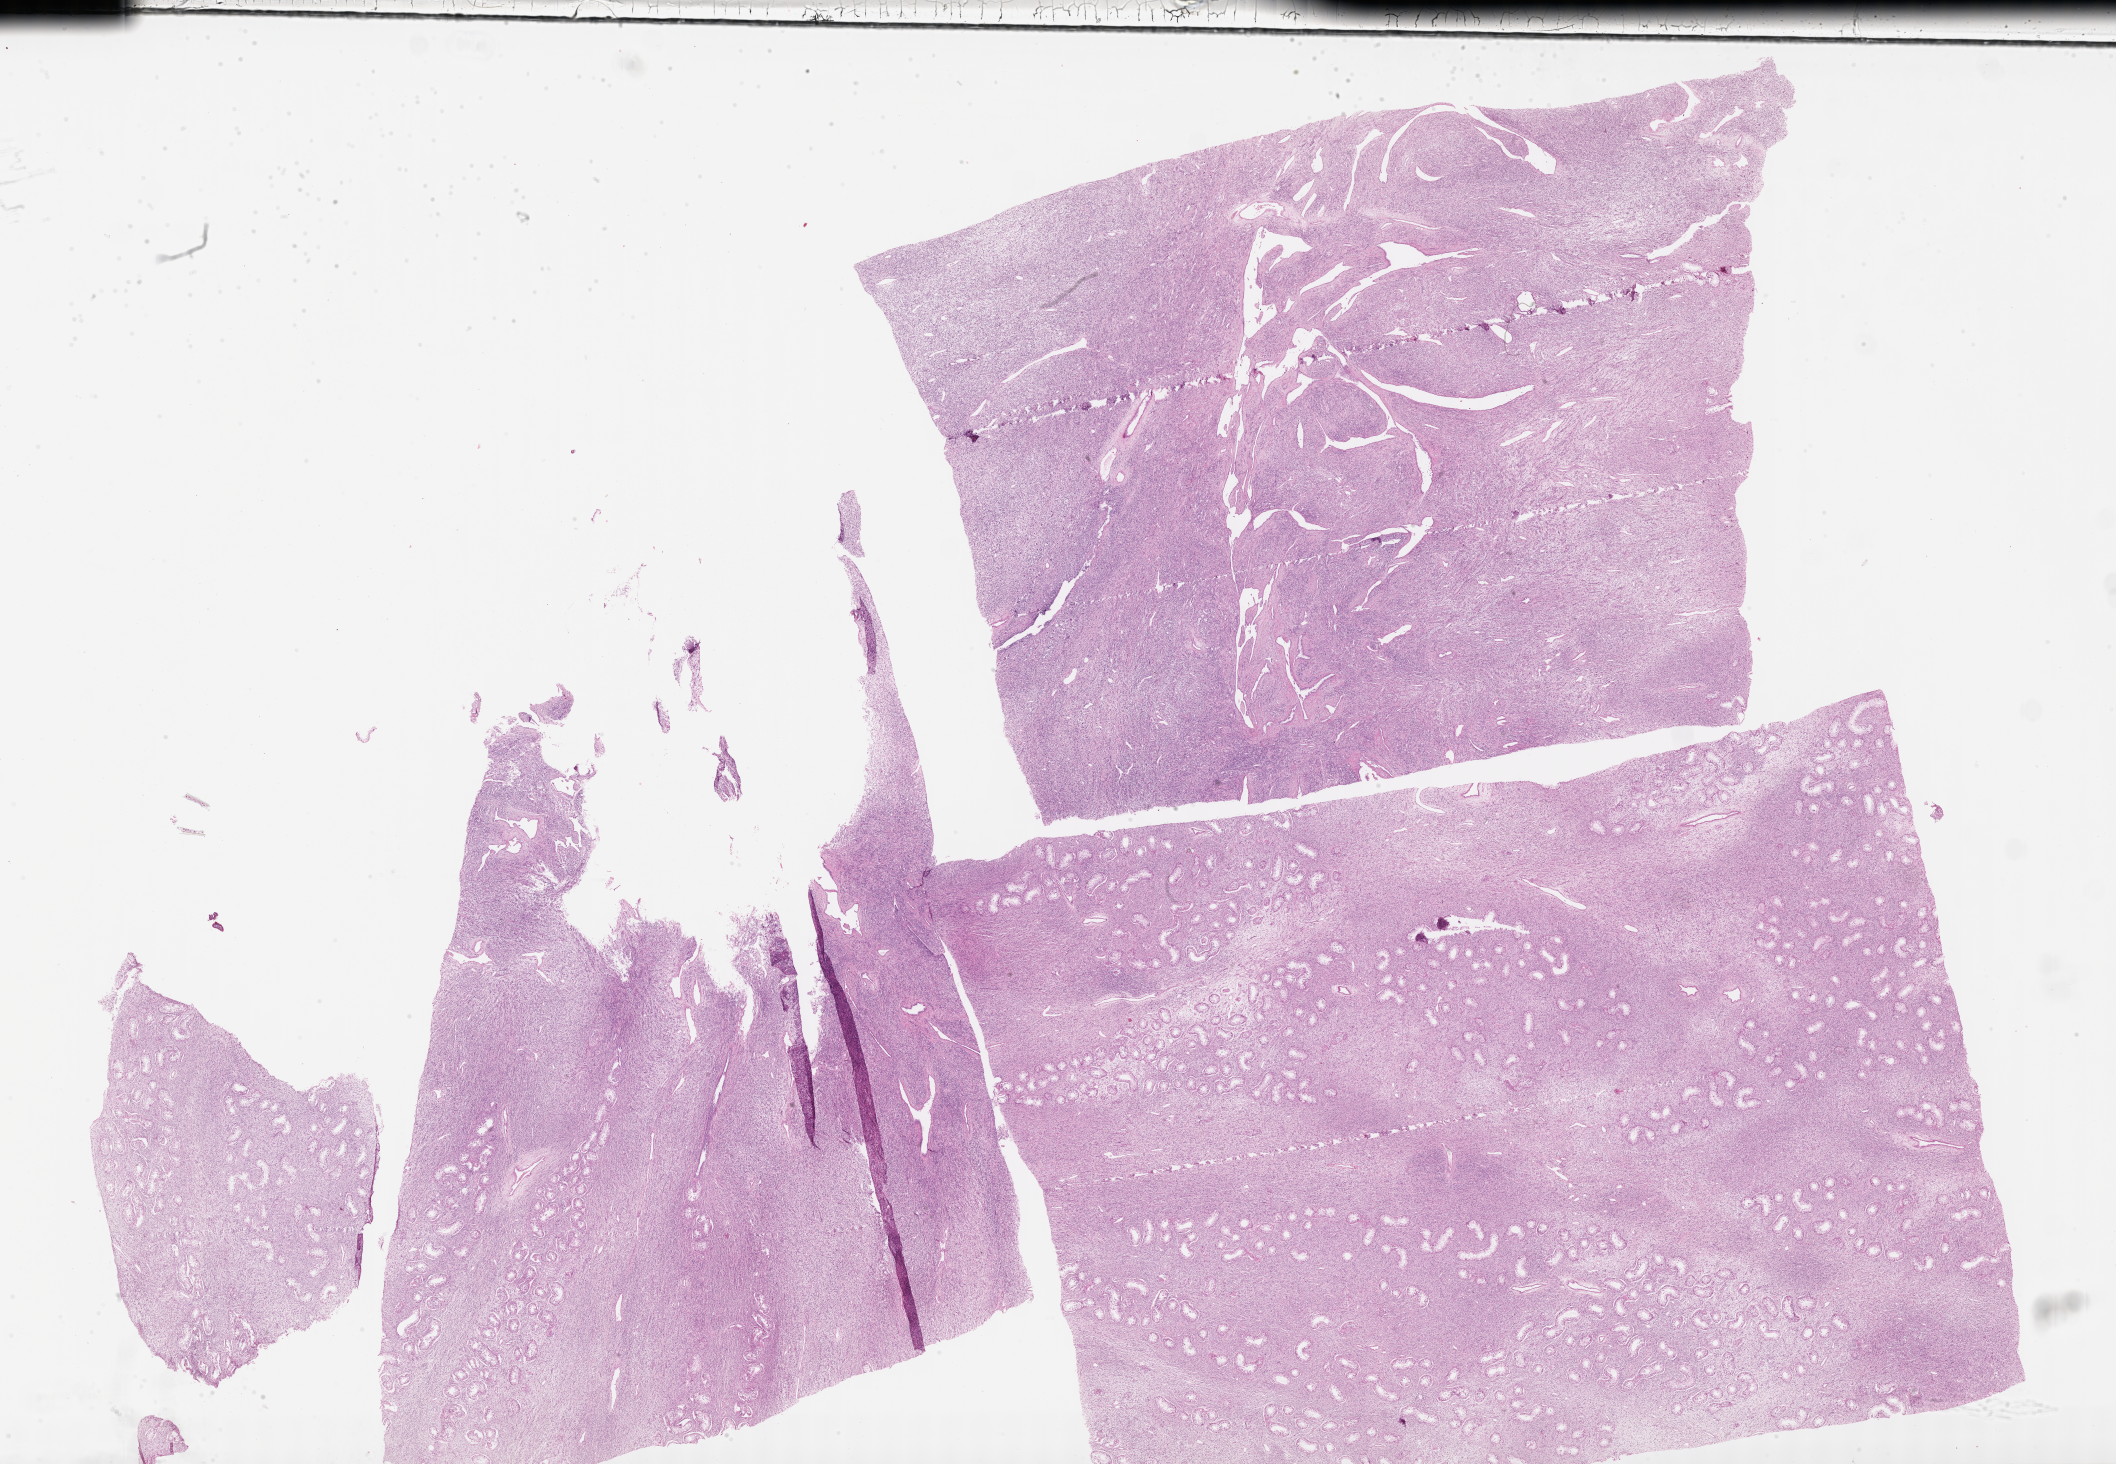
Digitized haematoxylin and eosin-stained section of tumor tissue, low-resolution overview of the scanned area, about 34.2 x 23.7 mm, formalin-fixed, paraffin-embedded (FFPE) tissue, sample anatomic site: testicle, right. Patient: male, age 14.5 years at diagnosis.
Diagnosis: rhabdomyosarcoma; histological classification: embryonal rhabdomyosarcoma.